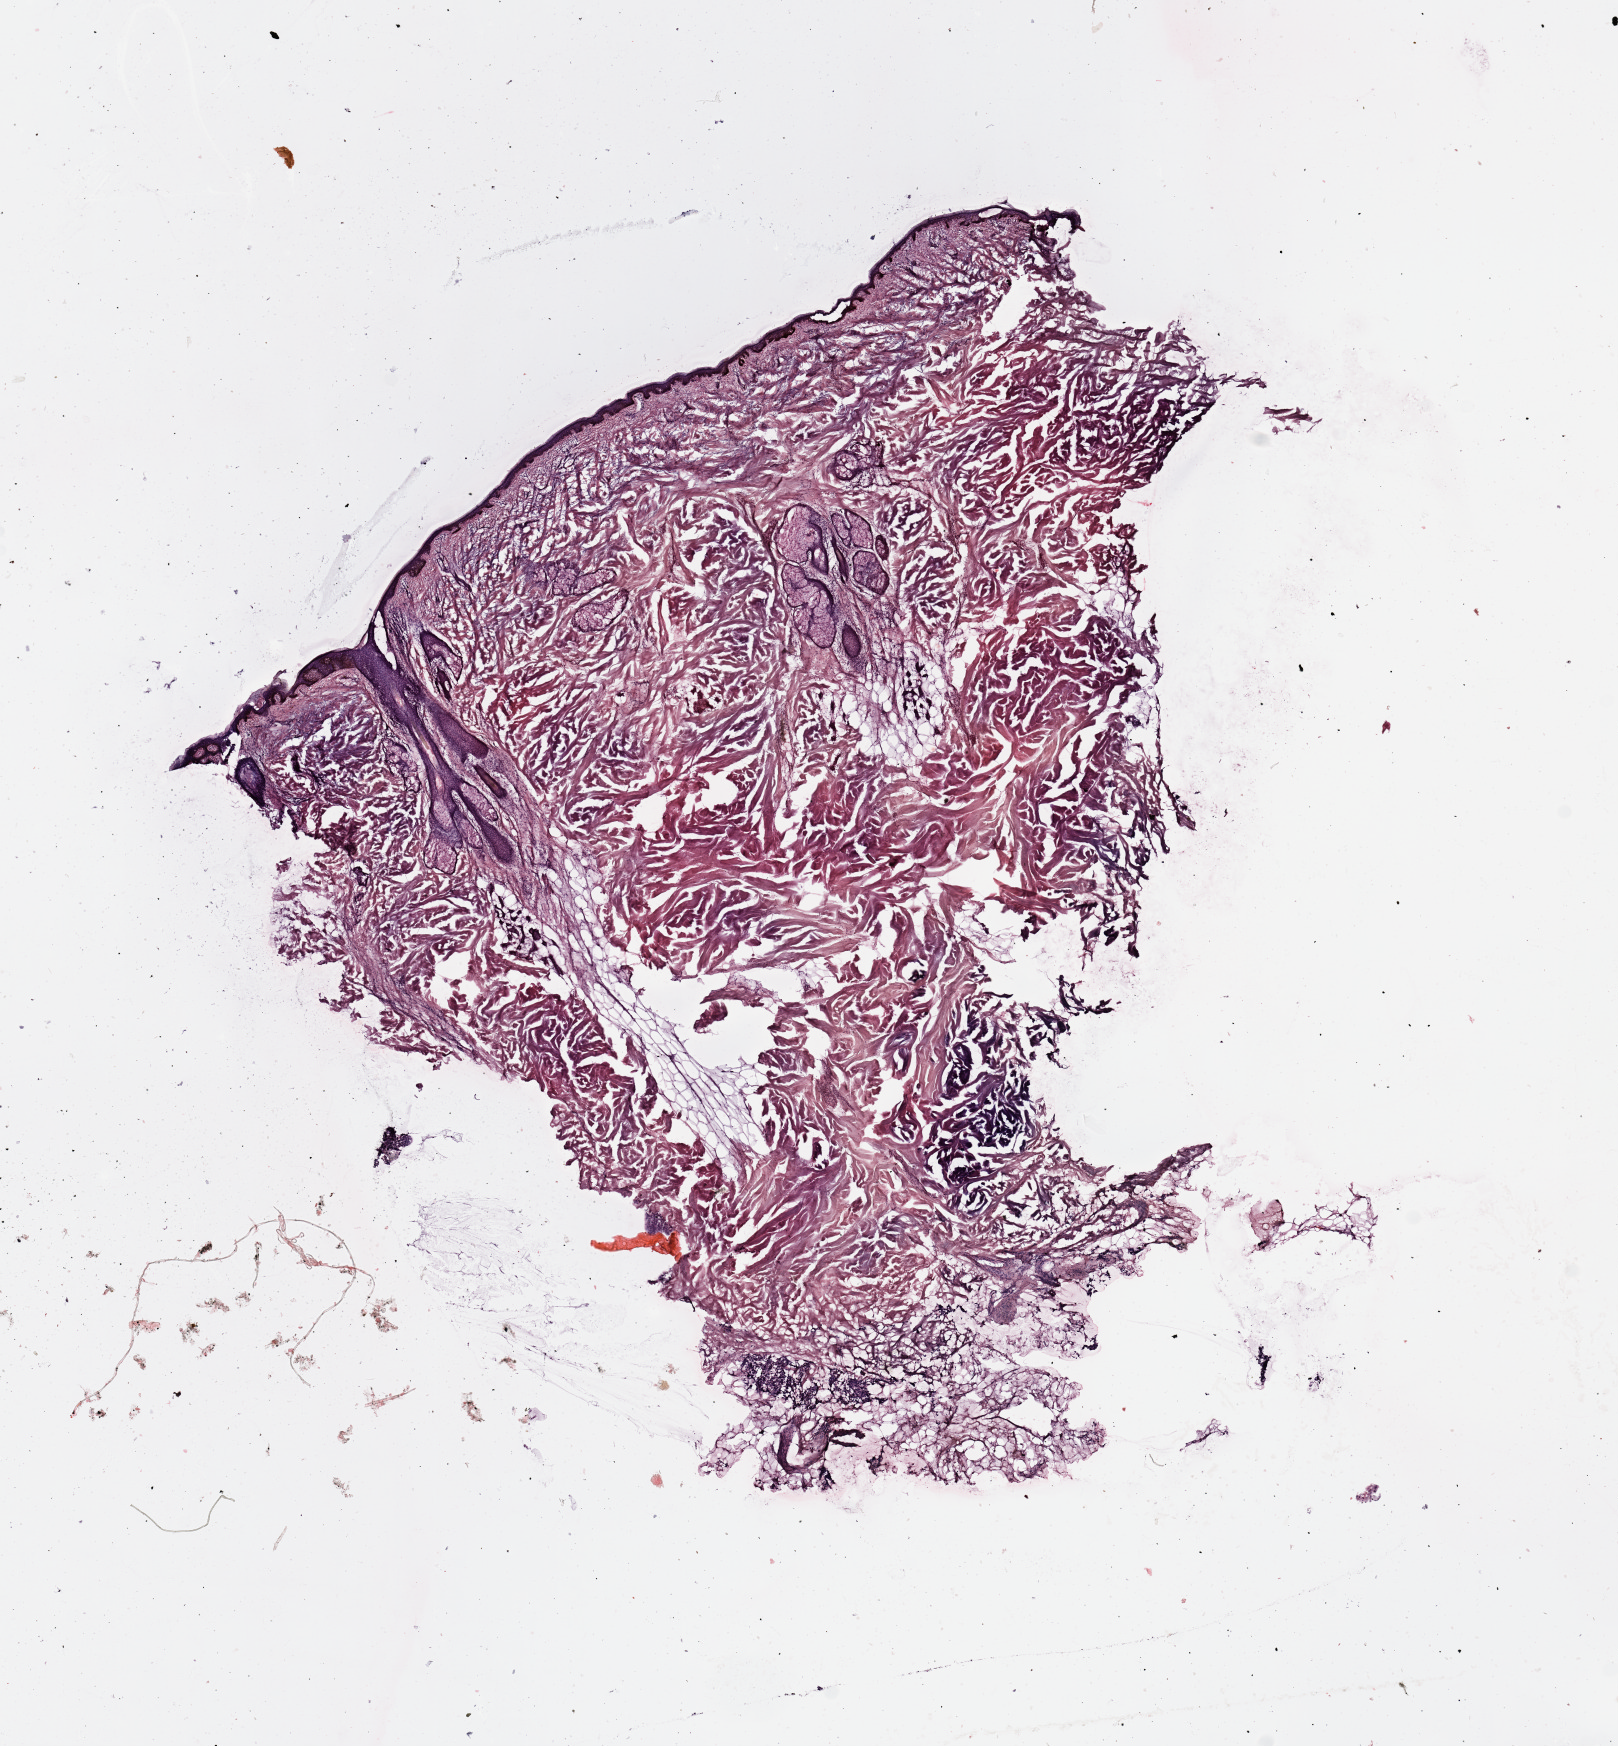
H&E-stained whole-slide image — a low-resolution overview of the entire scanned area, about 12.8 x 13.8 mm. Normal (non-tumour) tissue (melanoma cohort); sampled site not recorded. 61-year-old male patient.
This section: normal (non-tumour) tissue from the same patient. Patient diagnosis (cohort enrolment): cutaneous melanoma (skin).